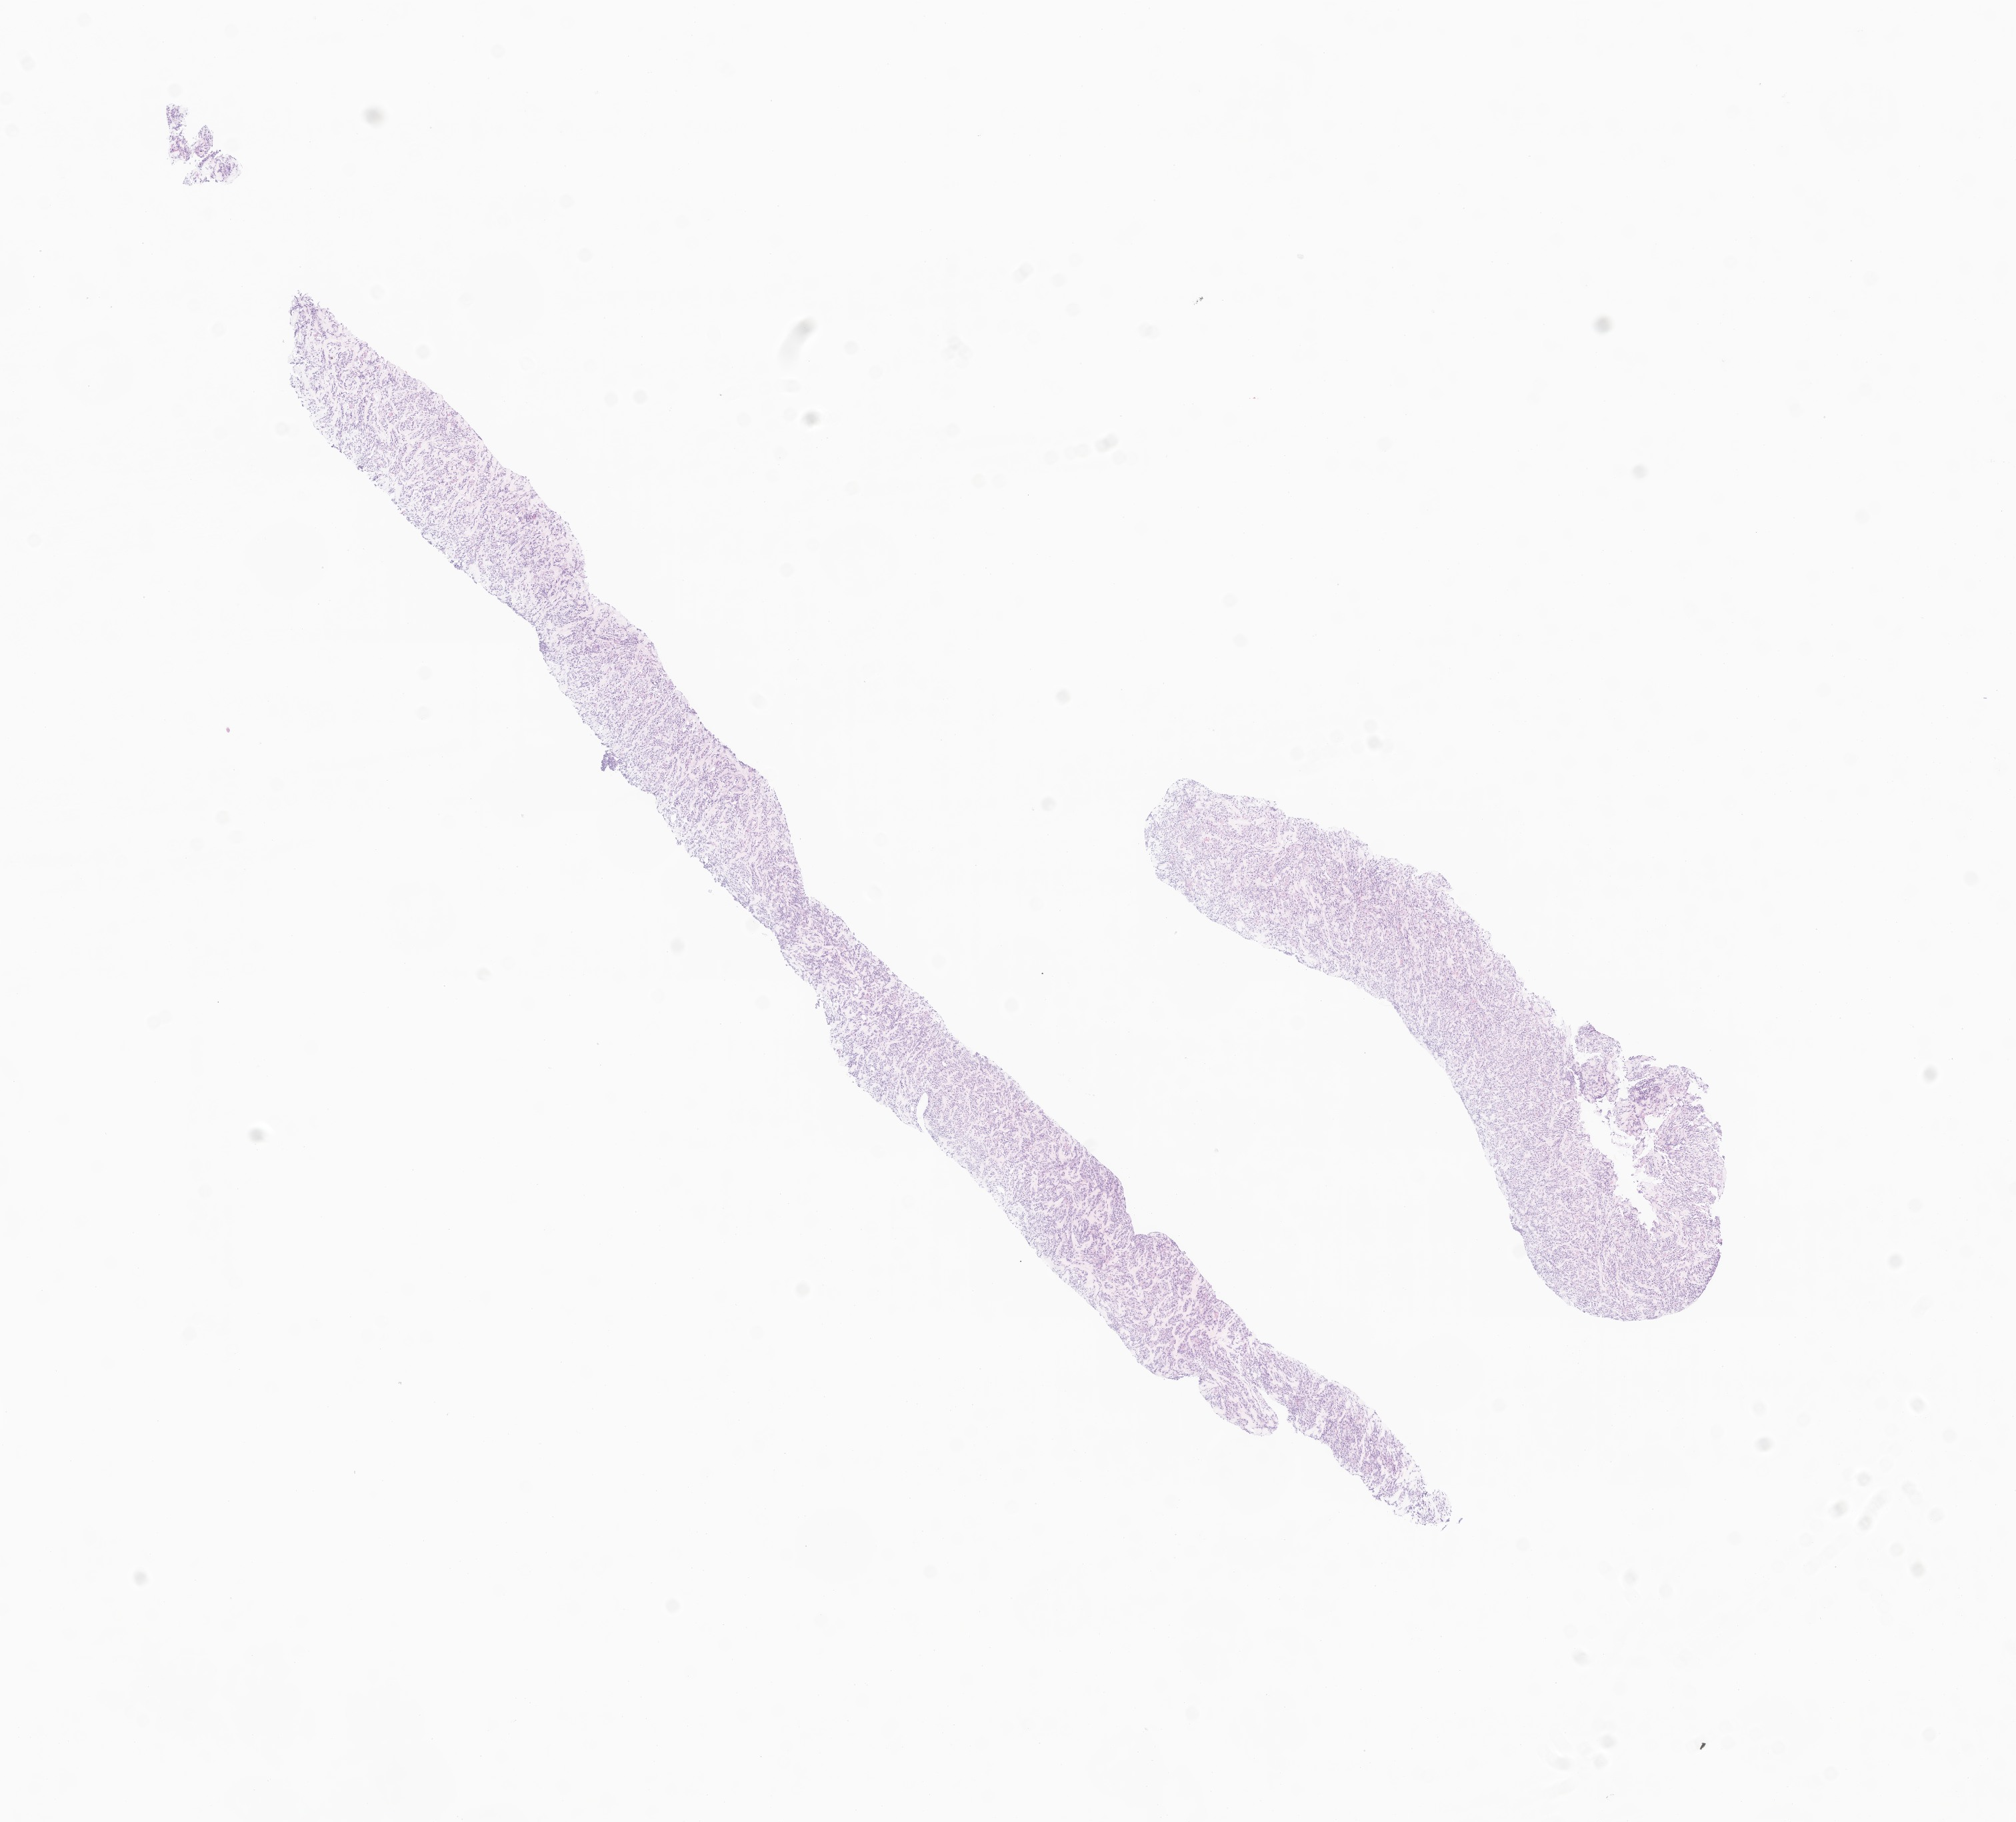
Whole-slide image, haematoxylin and eosin stain of tumor tissue from the head and neck, whole scanned area (about 12.7 x 11.5 mm) shown as a low-resolution overview; formalin-fixed, paraffin-embedded (FFPE) tissue. Patient: male, age 208 months (17 years 4 months).
Tissue or organ of origin (case record): head, face or neck. Recorded diagnosis: Rhabdomyosarcoma, NOS.